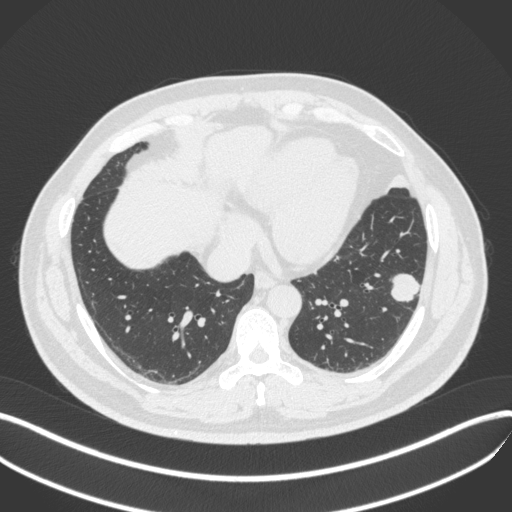
Chest CT, one axial slice. Position 141 of 420 along the scan axis. Reconstruction kernel B31f. Lung window (W 1500 / L -600 HU). 512 × 512 image matrix. Patient: male, 39 years. From the clinical record (not read from this slice): clinical TNM (as recorded): T2a N0 M0; histopathological grade: G2-3.
Structures marked on this image (rectangle marked by the reading radiologist):
- lung tumour (recorded histology: adenocarcinoma): bounding box <387,268,423,306> (left, top, right, bottom; pixels)